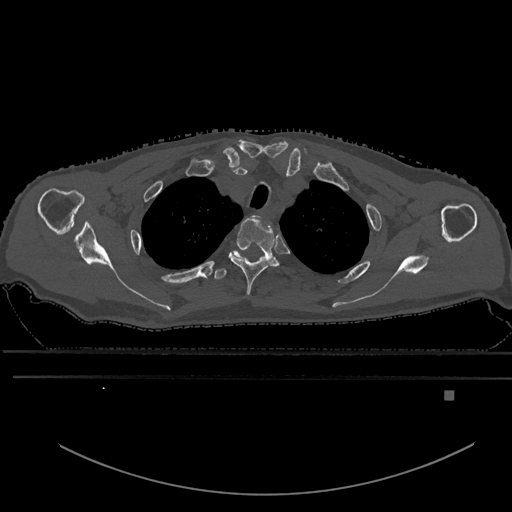
CT including the spine, one axial slice. Slice 490 of 969 in the series (ordered by position). Bone window (W 1800 / L 400 HU). 0.5 mm slice thickness. 512 × 512 image matrix, field of view 456 × 456 mm. Patient: male, 82 years. Case-level facts recorded for this patient, not image findings: primary cancer: prostate.
Annotated regions visible in this slice (semi-automatic segmentation, software-assisted and operator-edited):
- T2 vertebra: box from (x=228, y=215) to (x=279, y=295) px
- T3 vertebra: (x=213, y=252)–(x=245, y=280)